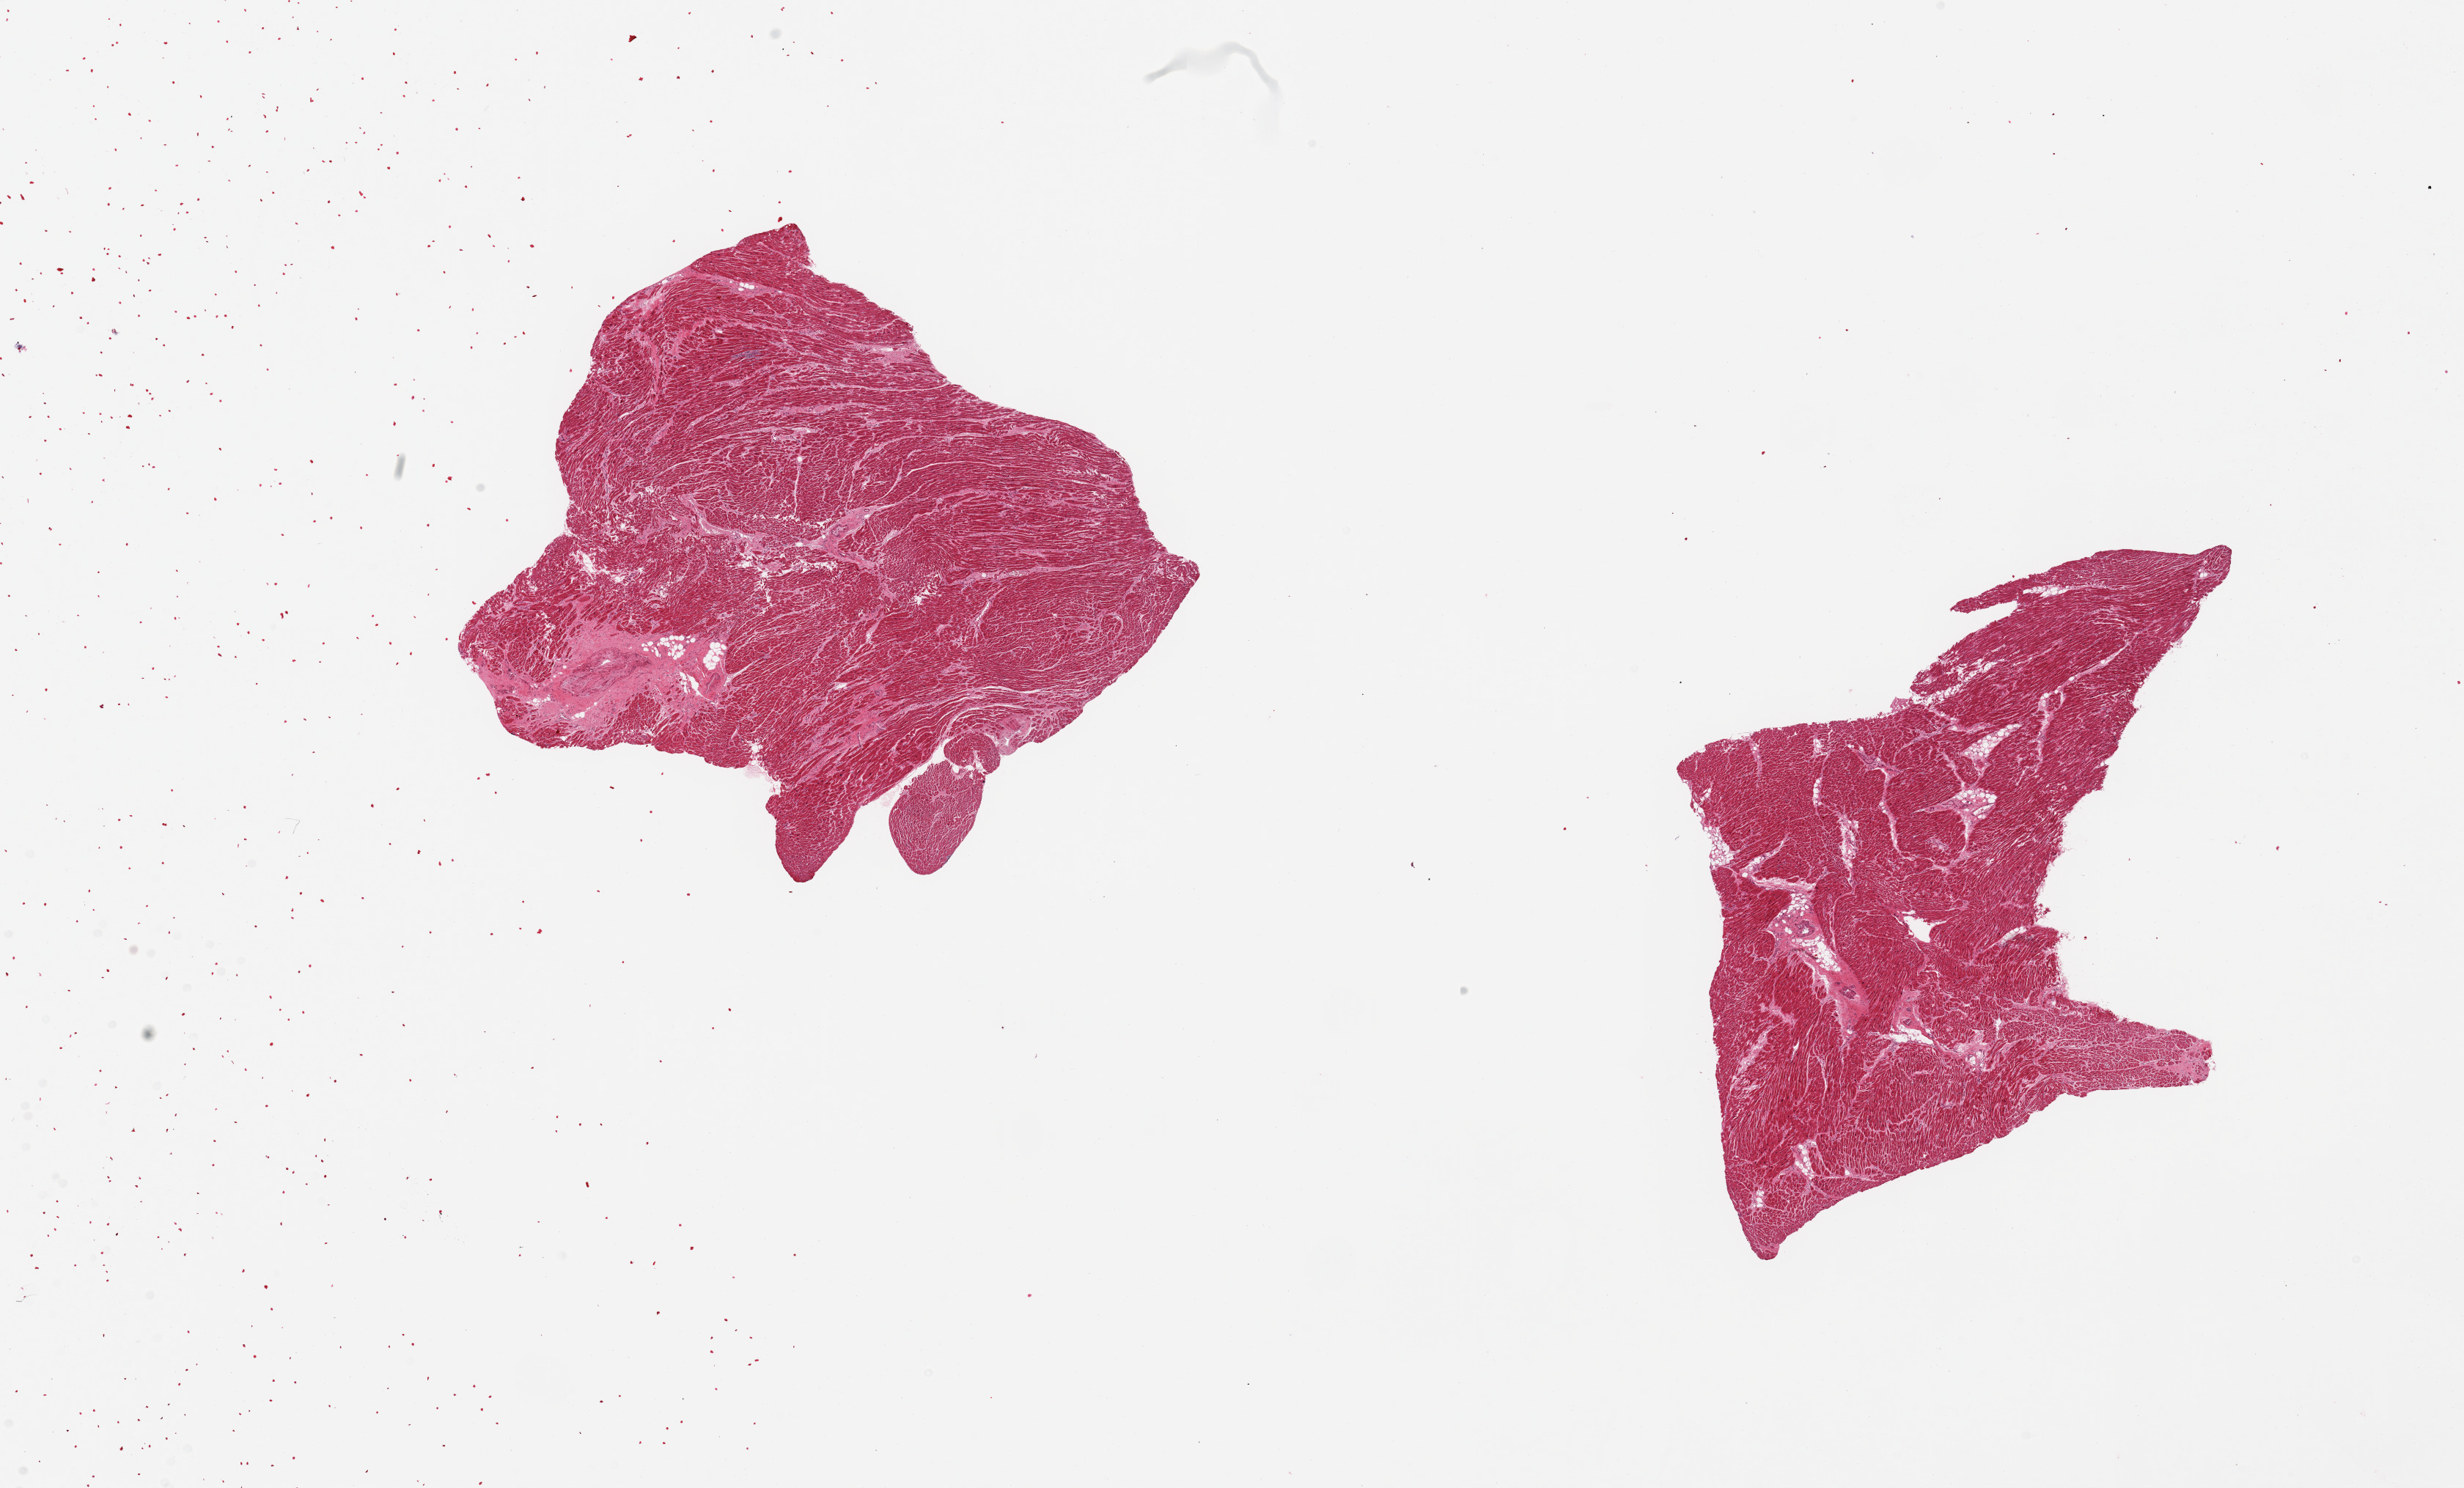
H&E whole-slide image — low-resolution overview of the scanned area, about 26.6 x 16.1 mm. PAXgene-fixed paraffin-embedded (PFPE) section. Section of heart (target tissue). Tissue donor sample. Male donor.
Review note (as recorded): 2 pieces; interstitial fibrosis with scarring and small amount of internal fat.